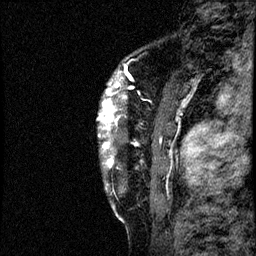
Breast MRI (dynamic contrast-enhanced), one sagittal slice. Position 10 of 60 along the scan axis. Dynamic contrast-enhanced study with each time point stored as its own series, time point 2 of 4 at this slice position (early post-contrast, ordered by acquisition time). 1.5 T. TE 4.2 ms, TR 17.6 ms. 2 mm slice thickness. 256 × 256 image matrix, field of view 200 × 200 mm. Female patient, age 40 years. From the clinical record (not read from this slice): setting: breast cancer imaged before/during neoadjuvant chemotherapy; receptor status: HER2-positive.
Outlined on this slice (semi-automatically segmented with operator editing):
- analysis volume of interest (the breast-tissue region the enhancement analysis was run in; not a lesion): box from (x=98, y=56) to (x=197, y=205) px
- tumour enhancement mask (voxels above the 100 % enhancement threshold inside the analysis volume of interest): (x=98, y=64)–(x=161, y=168)